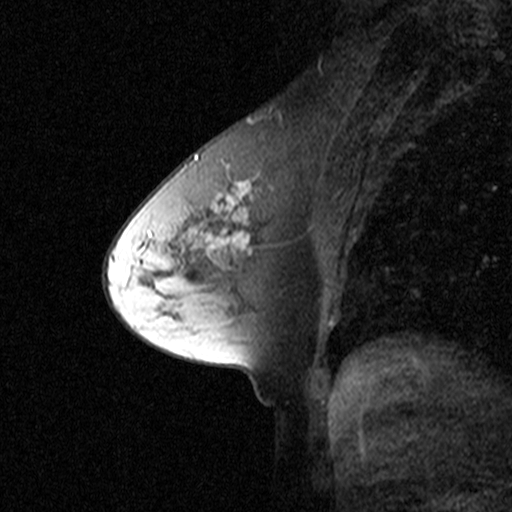
Breast MRI (dynamic contrast-enhanced), one sagittal slice; position 21 of 44 along the scan axis; dynamic contrast-enhanced study with each time point stored as its own series, time point 2 of 3 at this slice position (early post-contrast, ordered by acquisition time); 1.5 T; TE 4.5 ms, TR 11 ms; 3 mm slice thickness; 512 × 512 image matrix, field of view 200 × 200 mm. Female patient, age 53 years. From the clinical record (not read from this slice): setting: breast cancer imaged before/during neoadjuvant chemotherapy; receptor status: HR-positive, HER2-negative.
Outlined on this slice (semi-automatic segmentation, software-assisted and operator-edited):
- analysis volume of interest (the breast-tissue region the enhancement analysis was run in; not a lesion): bounding box [x1, y1, x2, y2] px = [170, 150, 277, 273]
- tumour enhancement mask (voxels above the 90 % enhancement threshold inside the analysis volume of interest): [194, 154, 252, 251]